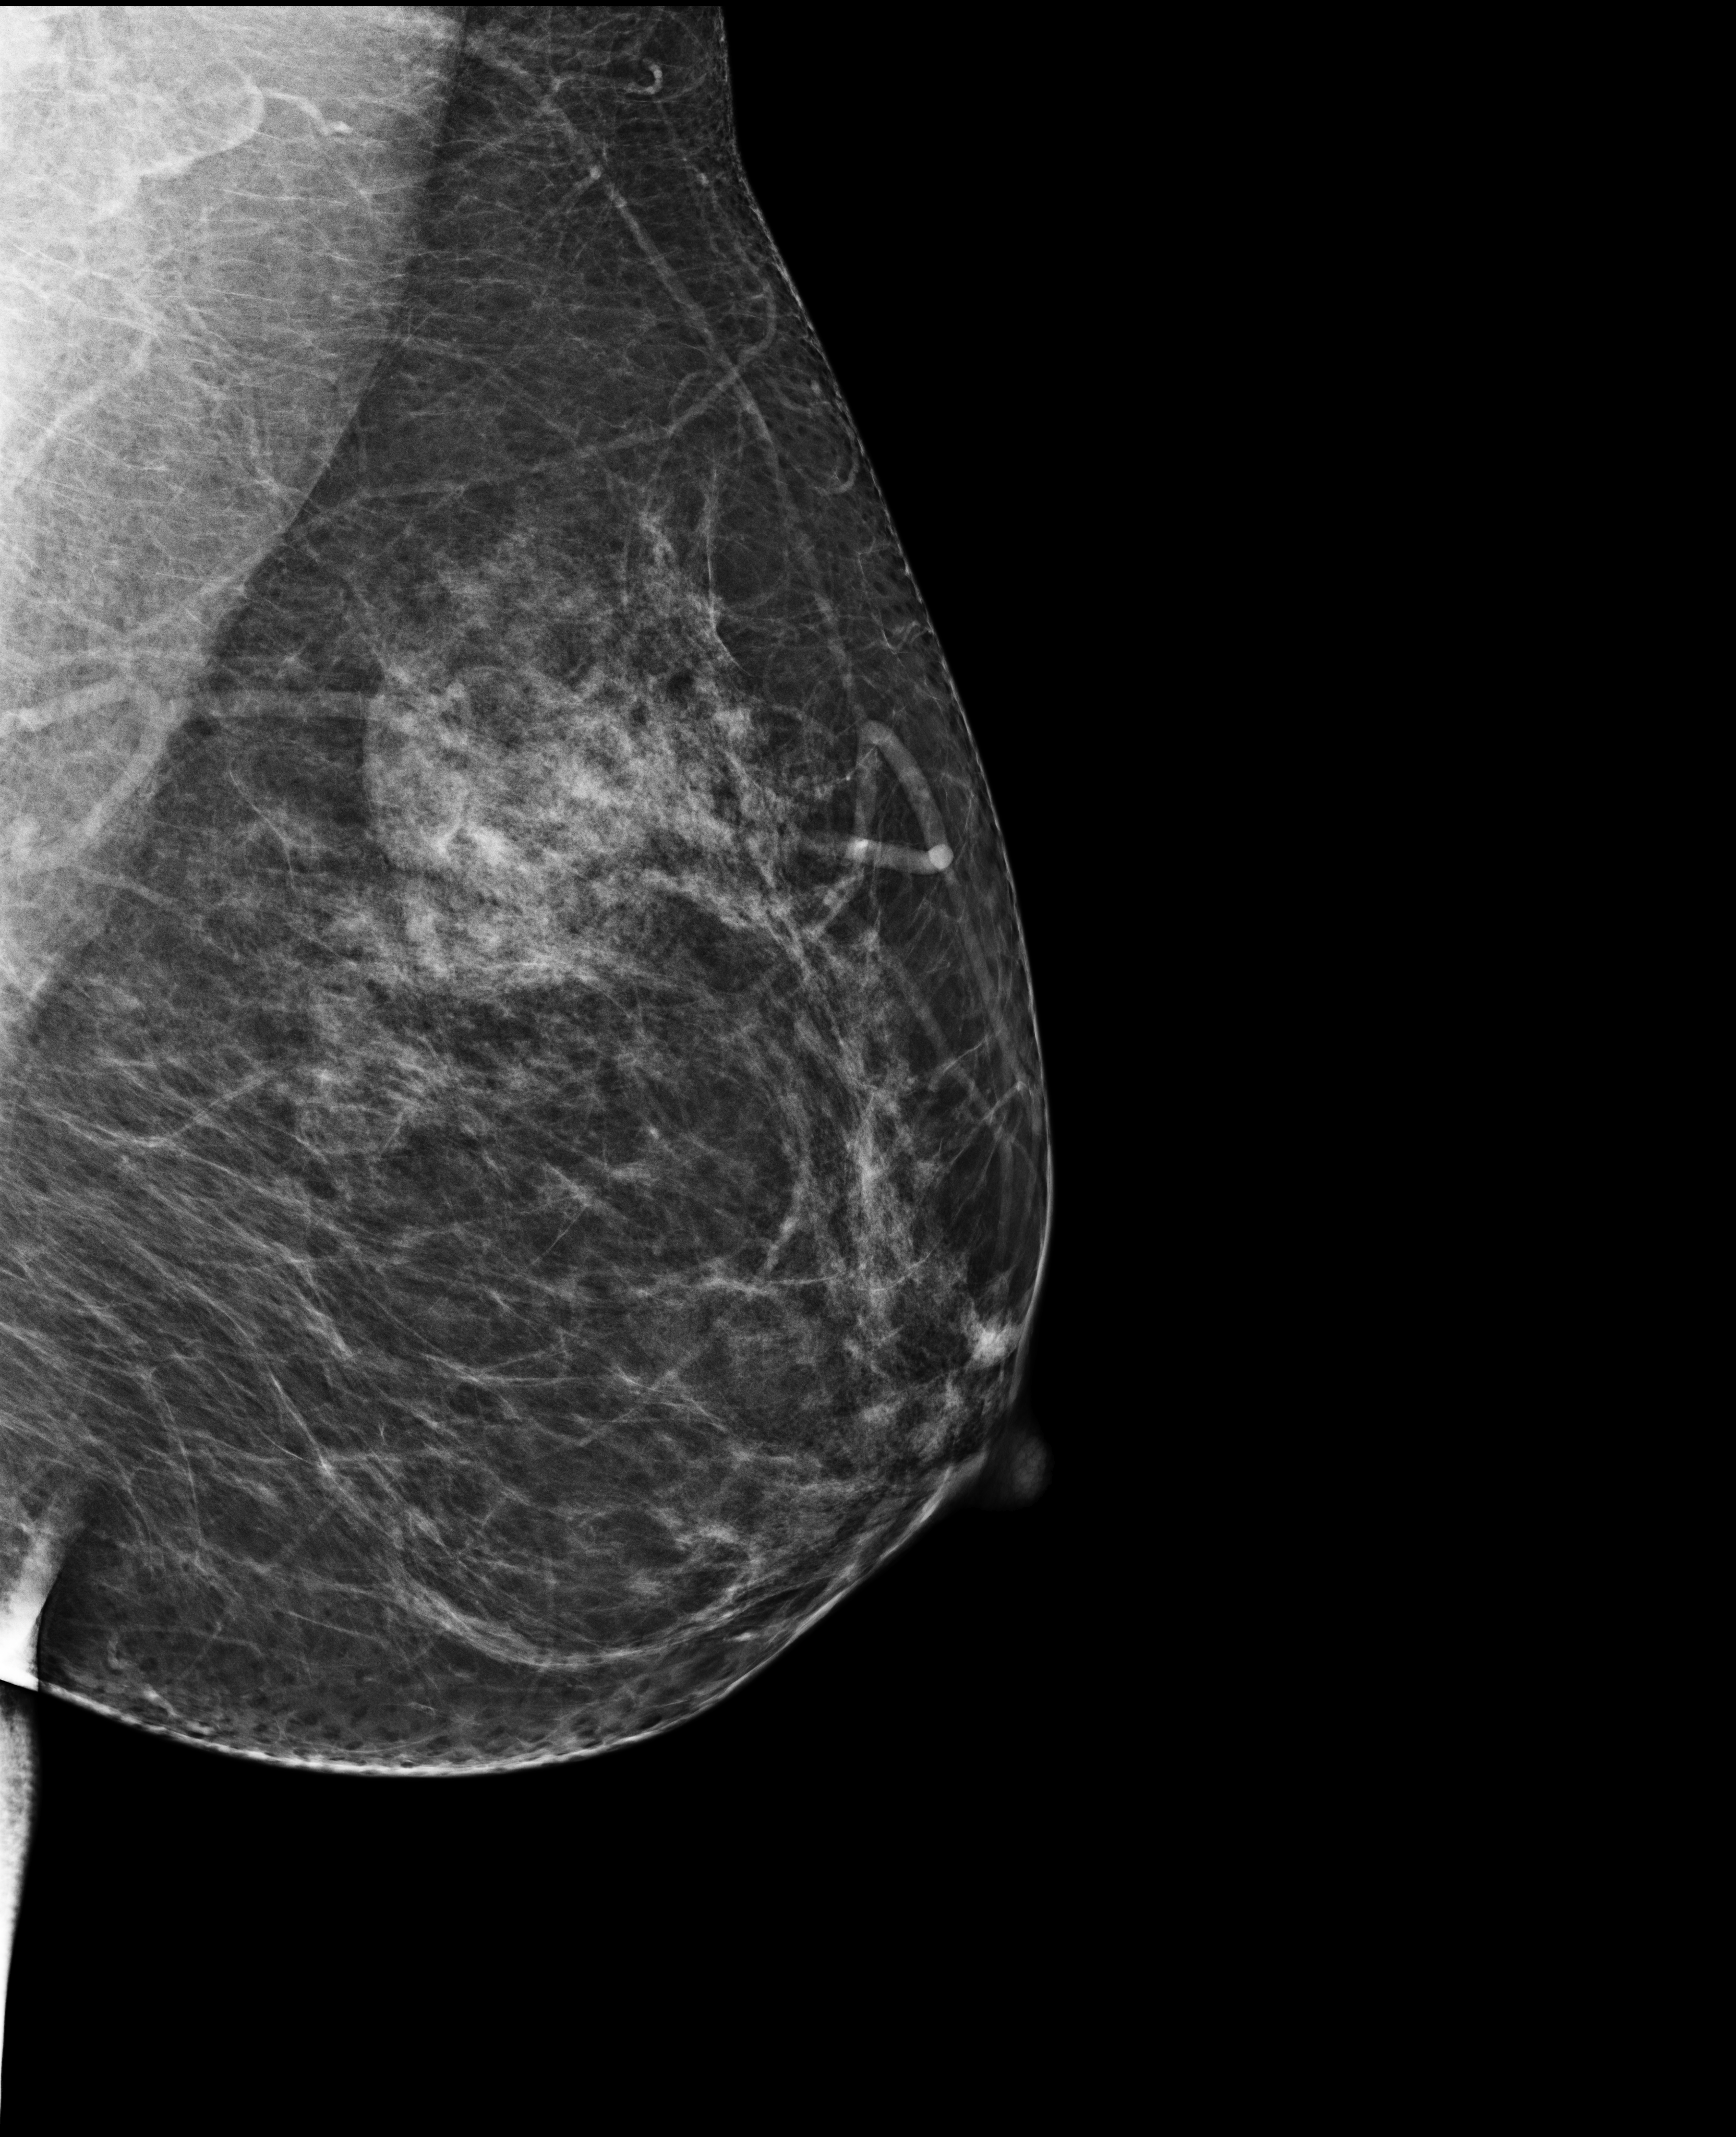
Screening examination, system: Selenia Dimensions. Patient: female, 48 years.
Image type: full-field digital mammogram. Breast: left. Projection: MLO view.